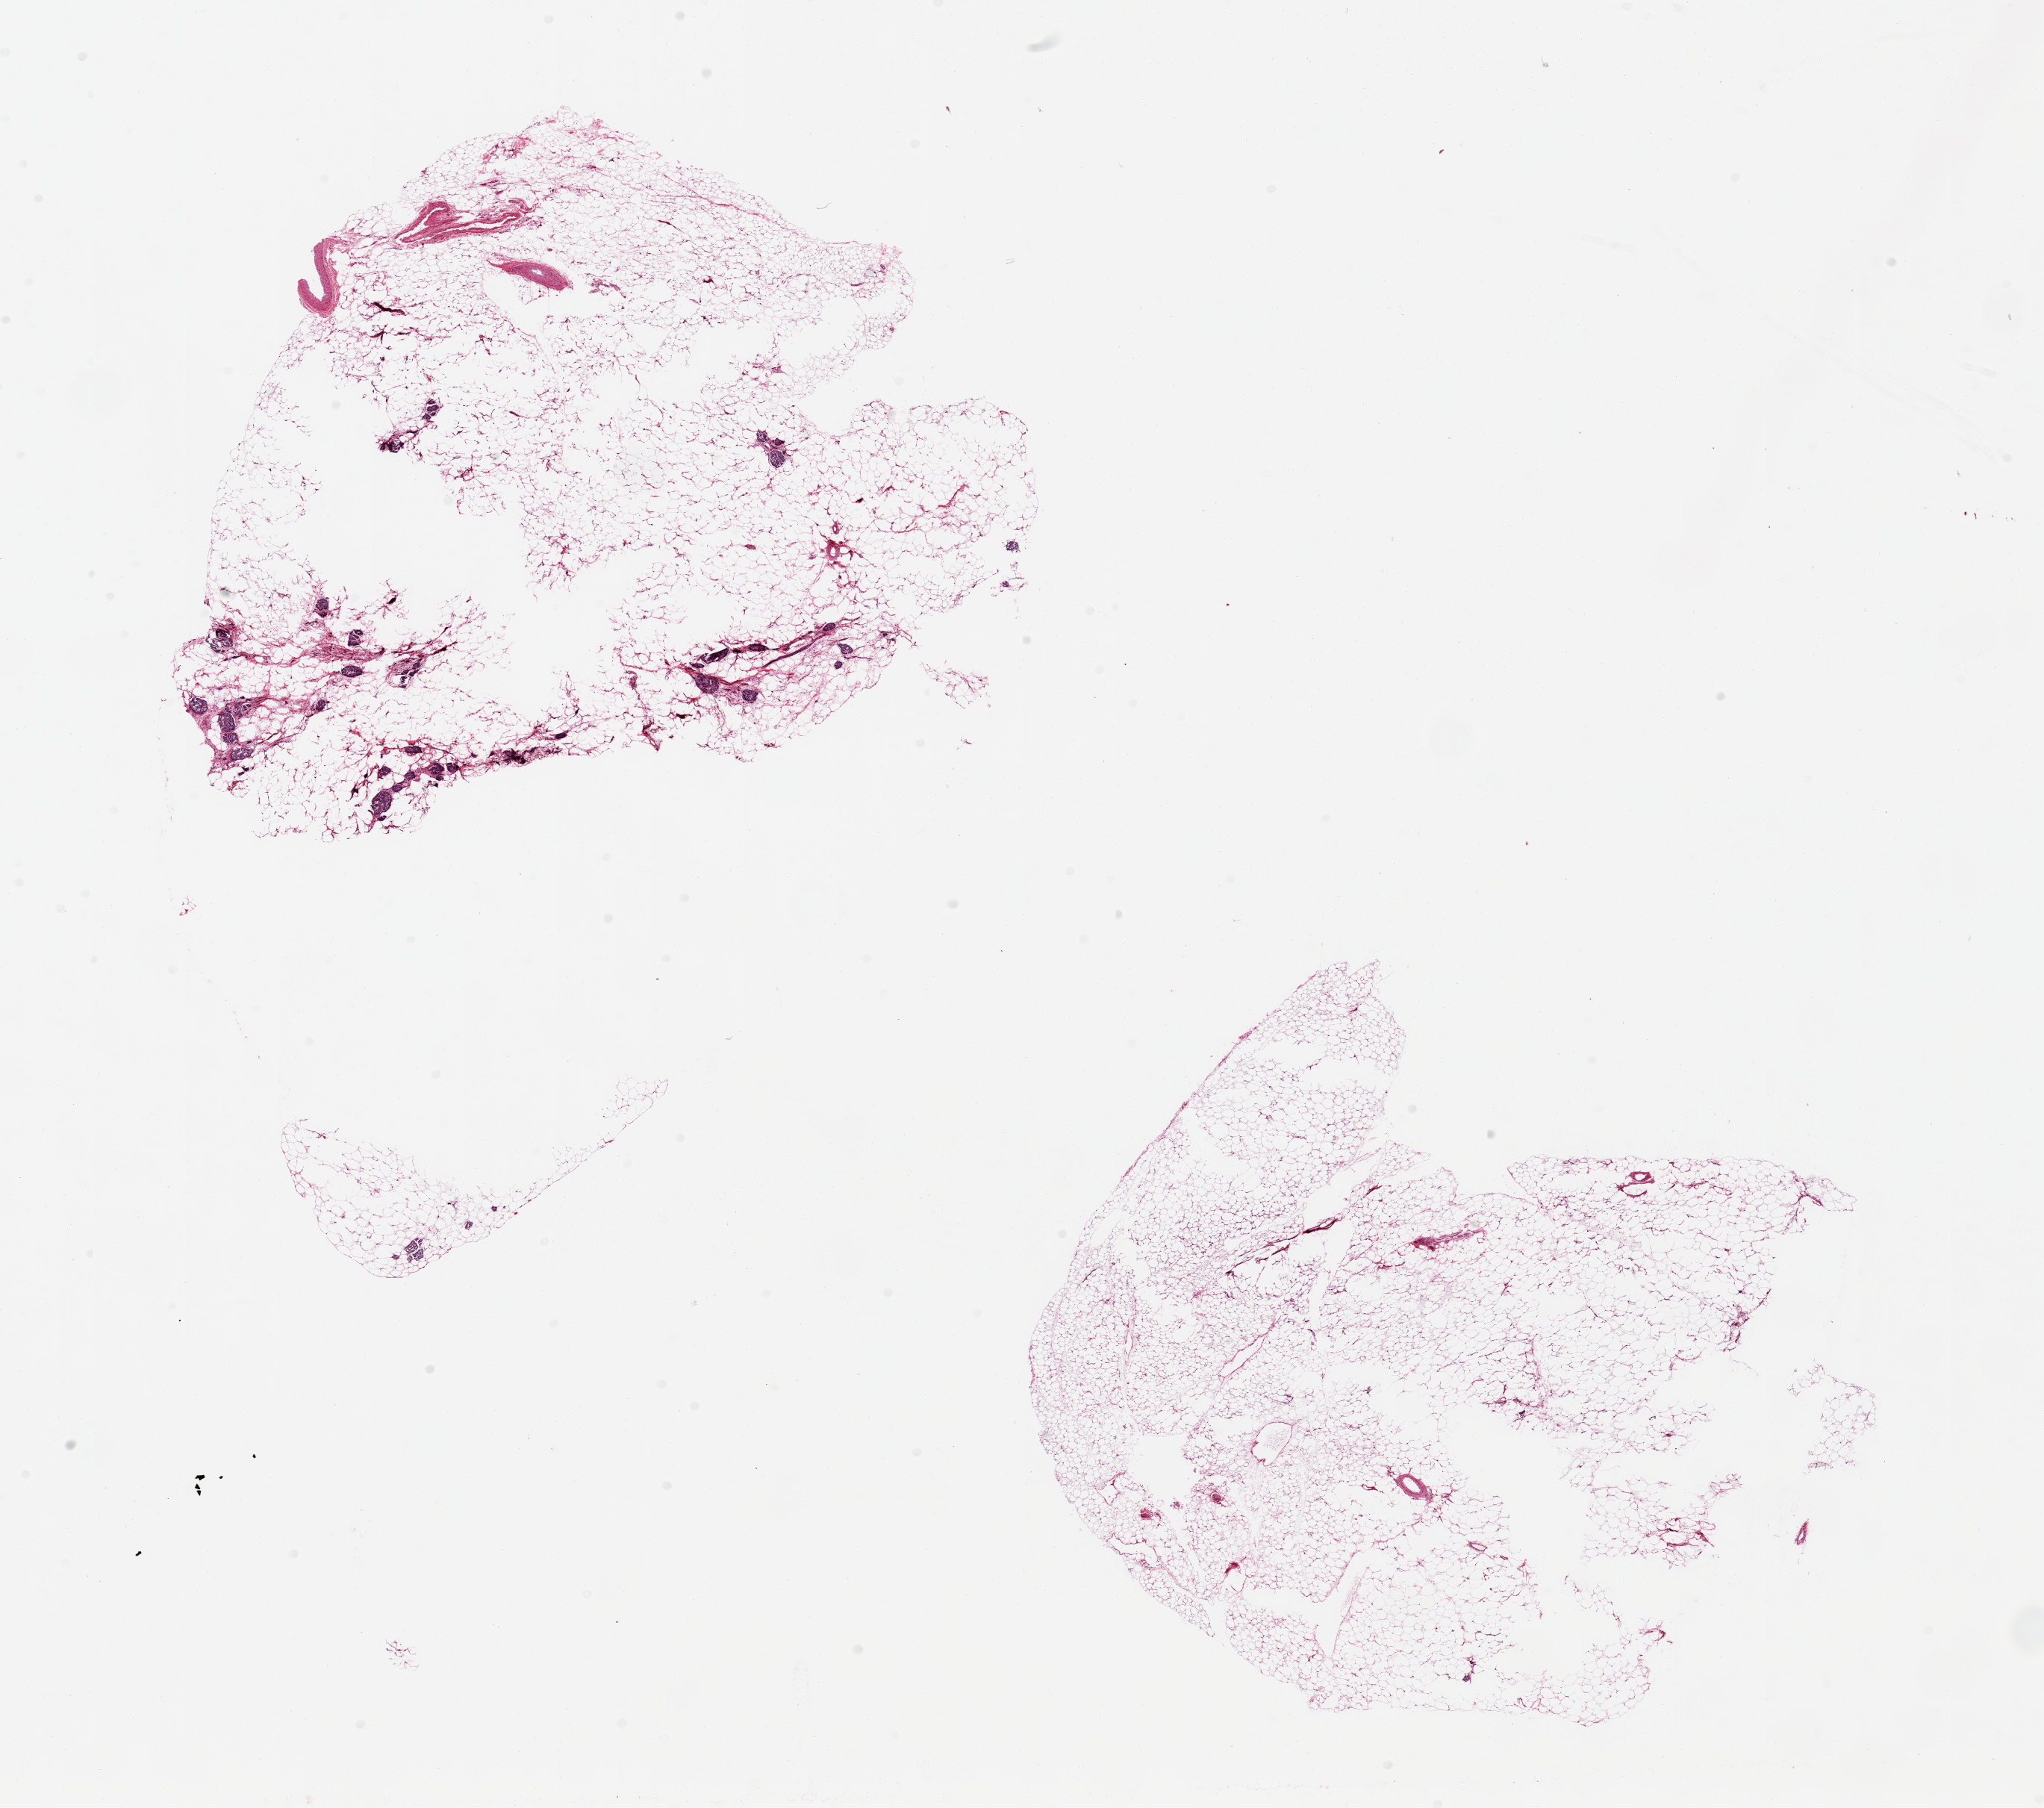
Whole-slide image, haematoxylin and eosin stain, low-resolution overview of the scanned area, about 21.7 x 19.2 mm; PAXgene-fixed paraffin-embedded (PFPE) section; section of pancreas (target tissue); donor tissue sample.
Pathologist's review note for this sample: 2 pieces, <5% pancreatic parenchyma, mainly fat.